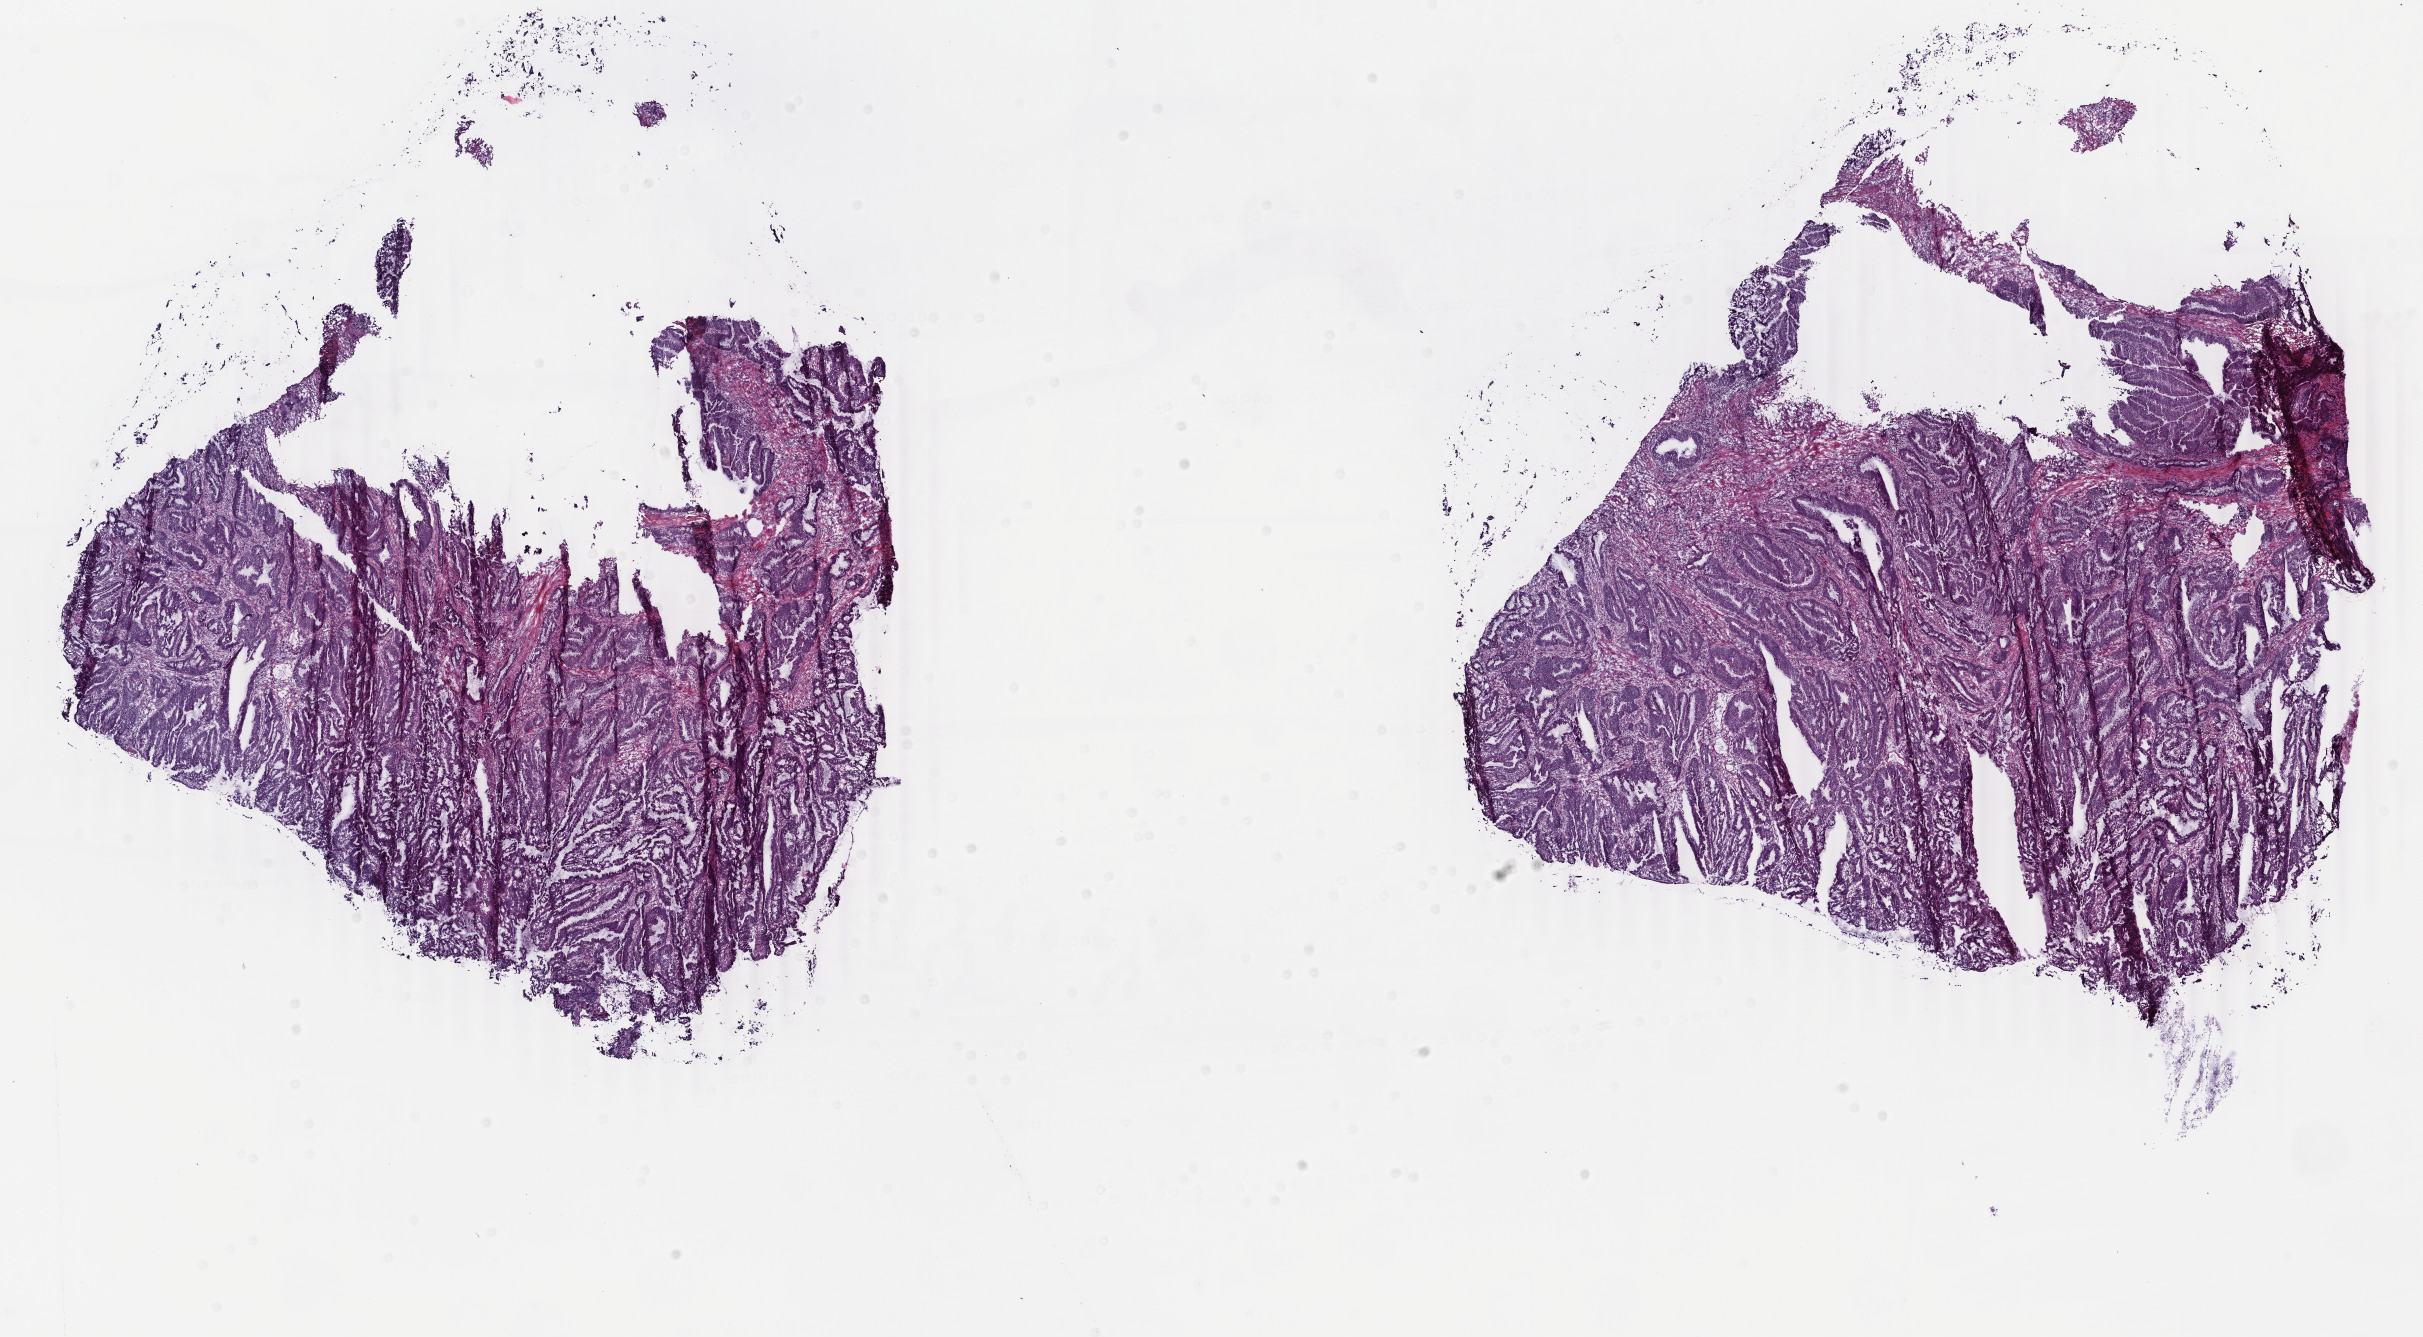
Digitized H&E tissue section (whole slide), shown as a low-resolution overview of the whole scanned area (about 19.3 x 10.6 mm, acquisition: 40x scan), frozen section from the bottom of the tissue portion, primary tumour sample from the colon. Male patient; age at initial diagnosis 82 years. Composition of this section per pathologist review: tumour cells 85%, tumour nuclei 80%.
Histologic diagnosis: Adenocarcinoma, NOS.